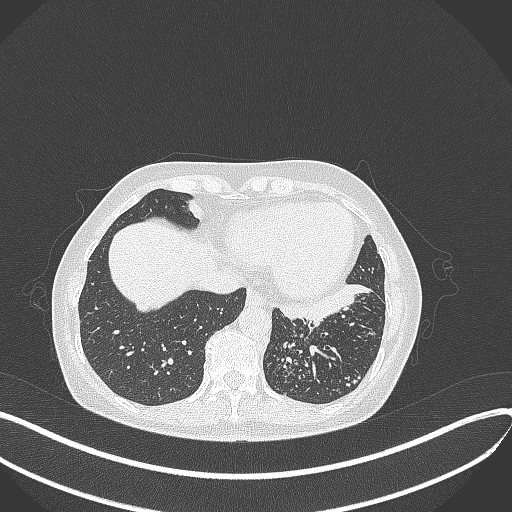
Chest CT, one axial slice; position 109 of 429 along the scan axis; 100 kVp; lung window (W 1500 / L -600 HU); 1 mm slice thickness; 512 × 512 image matrix, field of view 400 × 400 mm. Patient: female, 63 years. Case-level facts recorded for this patient, not image findings: clinical TNM (as recorded): T1b N0 M0; histopathological grade: G2-3.
Outlined on this slice (rectangle marked by the reading radiologist):
- lung tumour (recorded histology: adenocarcinoma): bounding box (x1, y1, x2, y2) in pixels: (283, 276, 375, 324)